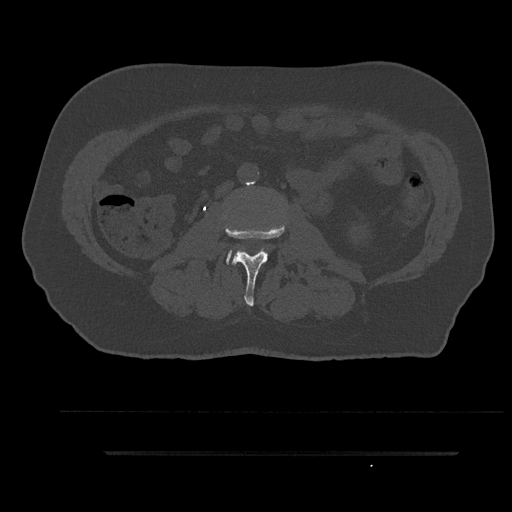
CT including the spine, one axial slice. Slice 85 of 797 in the series (ordered by position). Reconstruction kernel Br40s/3. Bone window (W 1800 / L 400 HU). 0.5 mm slice thickness. 512 × 512 image matrix, field of view 432 × 432 mm. Patient: male, 63 years. Case-level facts recorded for this patient, not image findings: primary cancer: renal; vertebrae with lytic lesions (as recorded): T8.
Structures marked on this image (semi-automatically segmented with operator editing):
- L2 vertebra: bounding box (x1, y1, x2, y2) in pixels: (224, 223, 285, 306)
- L3 vertebra: (226, 251, 242, 264)